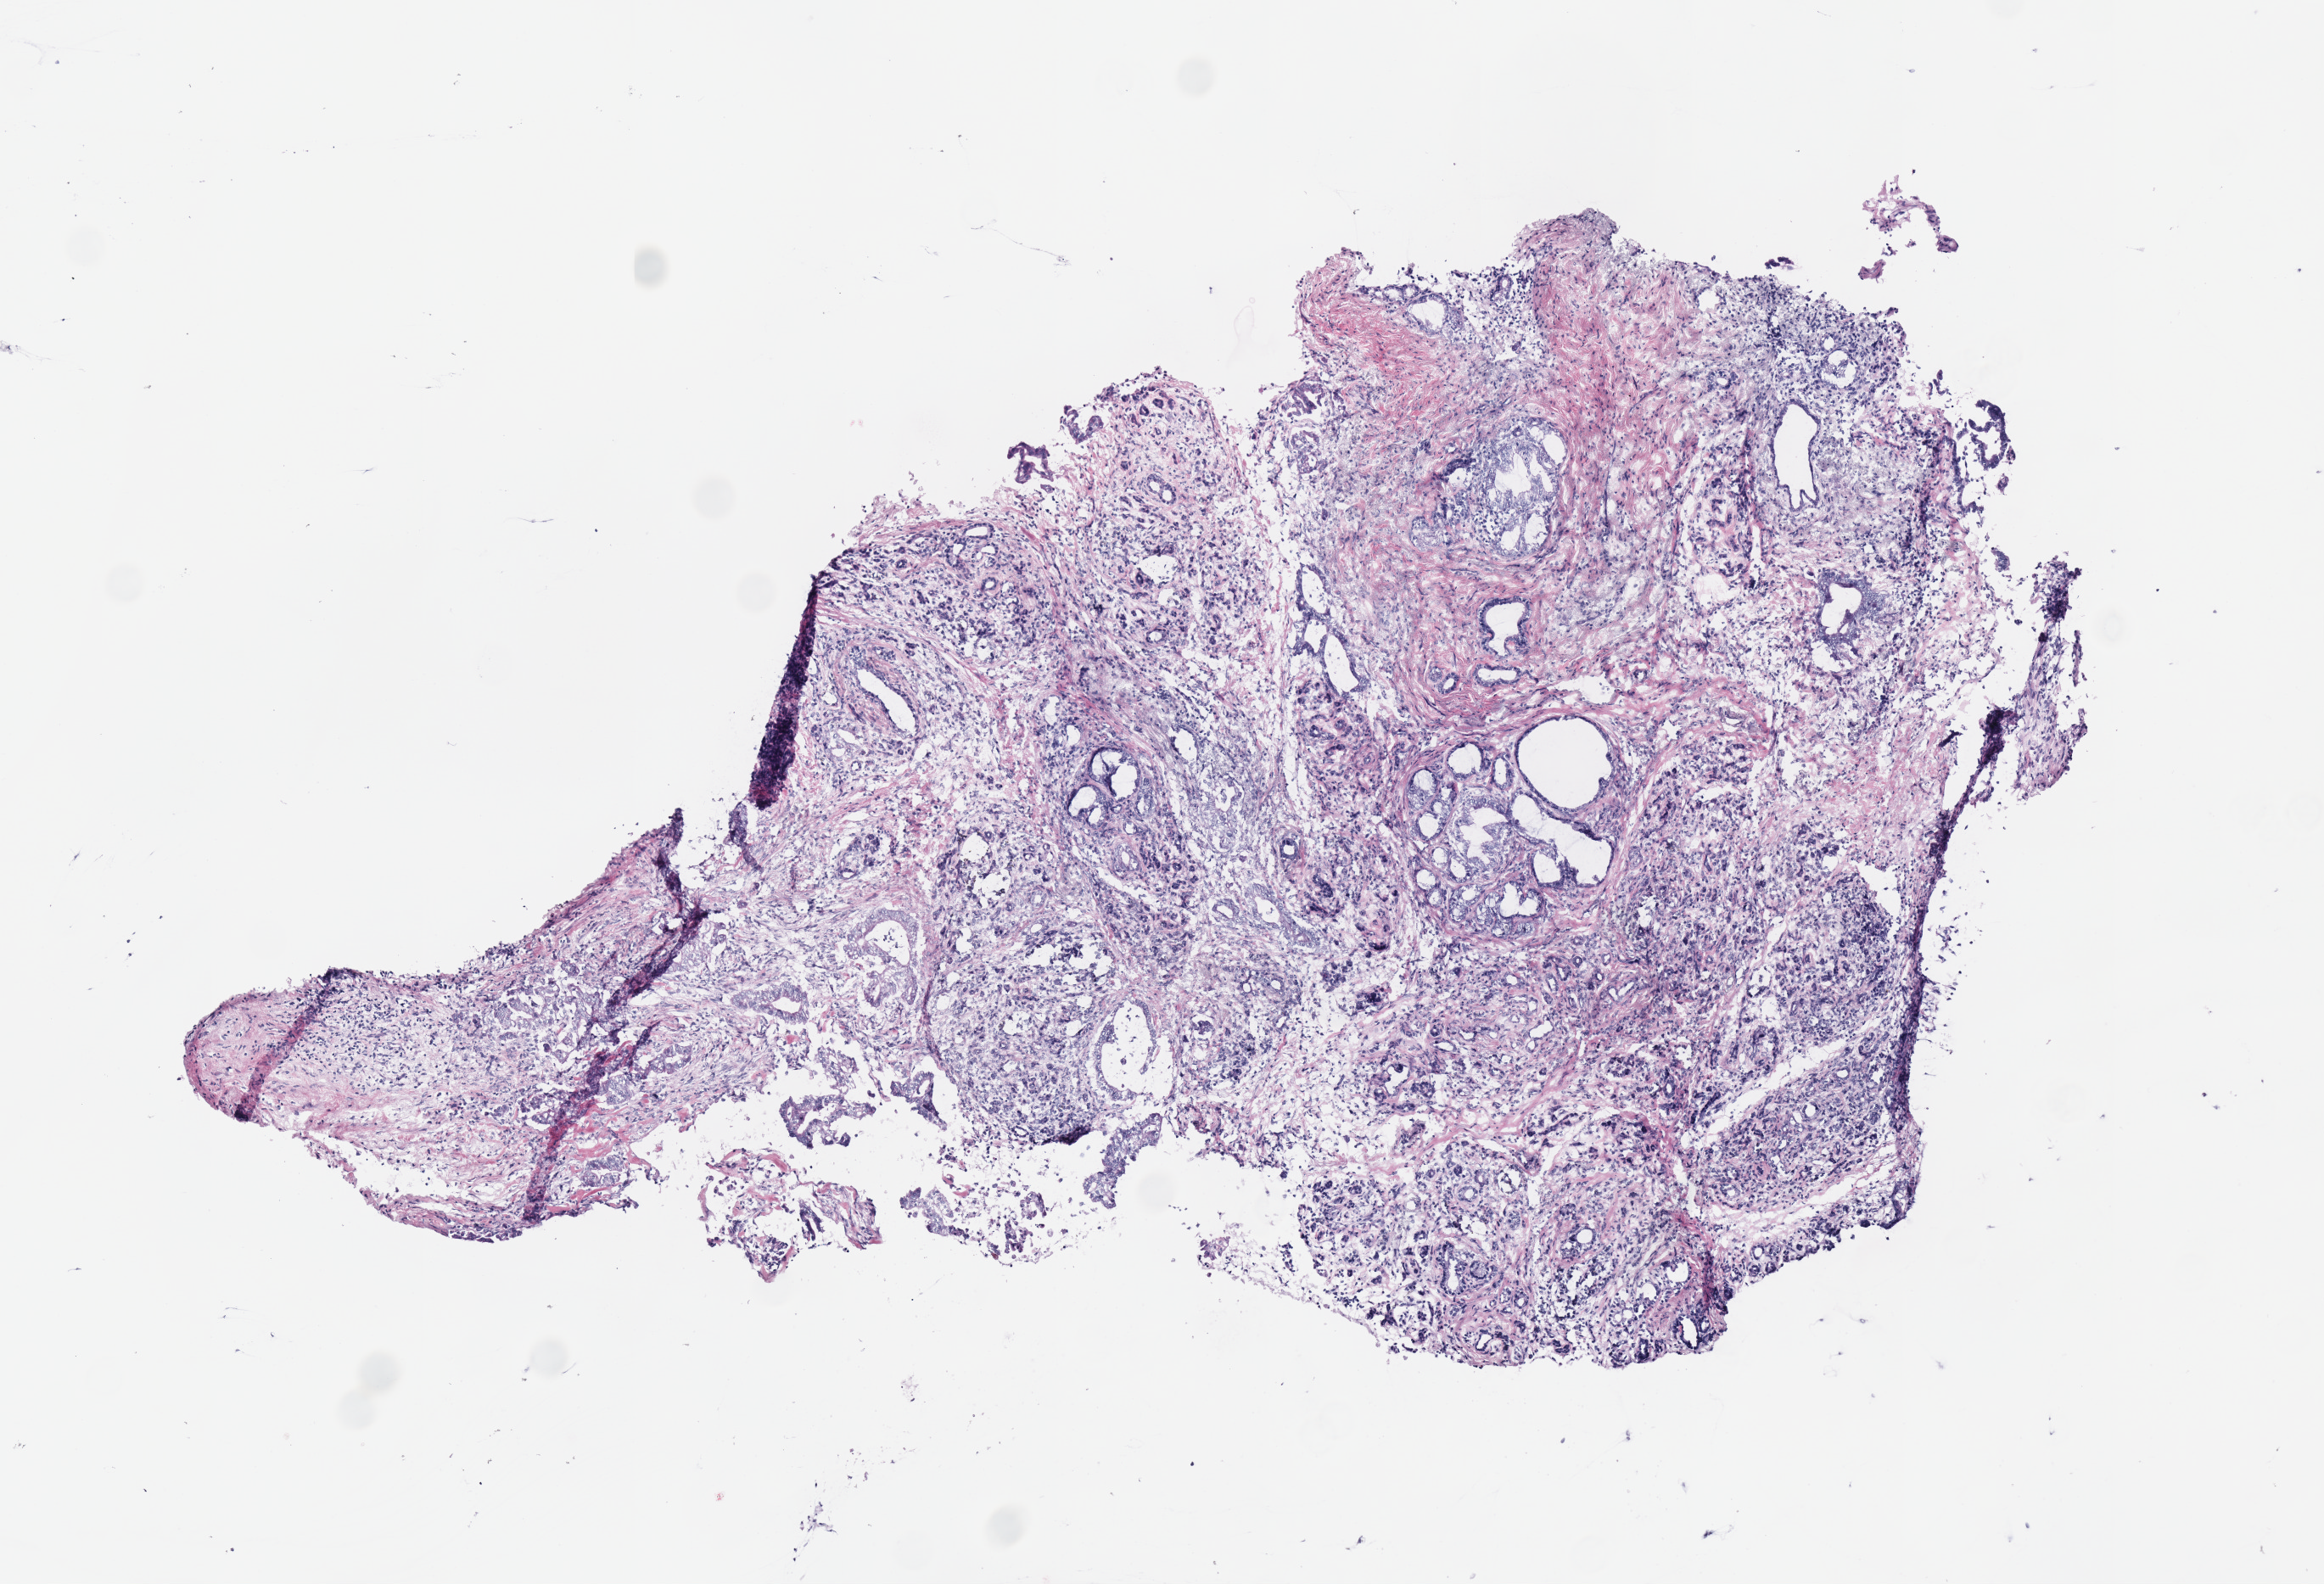
H&E whole-slide image, whole scanned area (about 5.4 x 3.7 mm, slide scanned at 40x) shown as a low-resolution overview, frozen section from the top of the tissue portion, sample: primary tumour, pancreas. Female, age 78 years at initial diagnosis. Histologic grade: G2 (moderately differentiated). Composition of this section per pathologist review: tumour cells 80%, tumour nuclei 75%, normal cells 0%, stromal cells 20%, necrosis 0%.
Lymph nodes positive (case pathology): 3 of 12 examined. AJCC pathologic stage: IIB. Diagnosis: Infiltrating duct carcinoma, NOS.